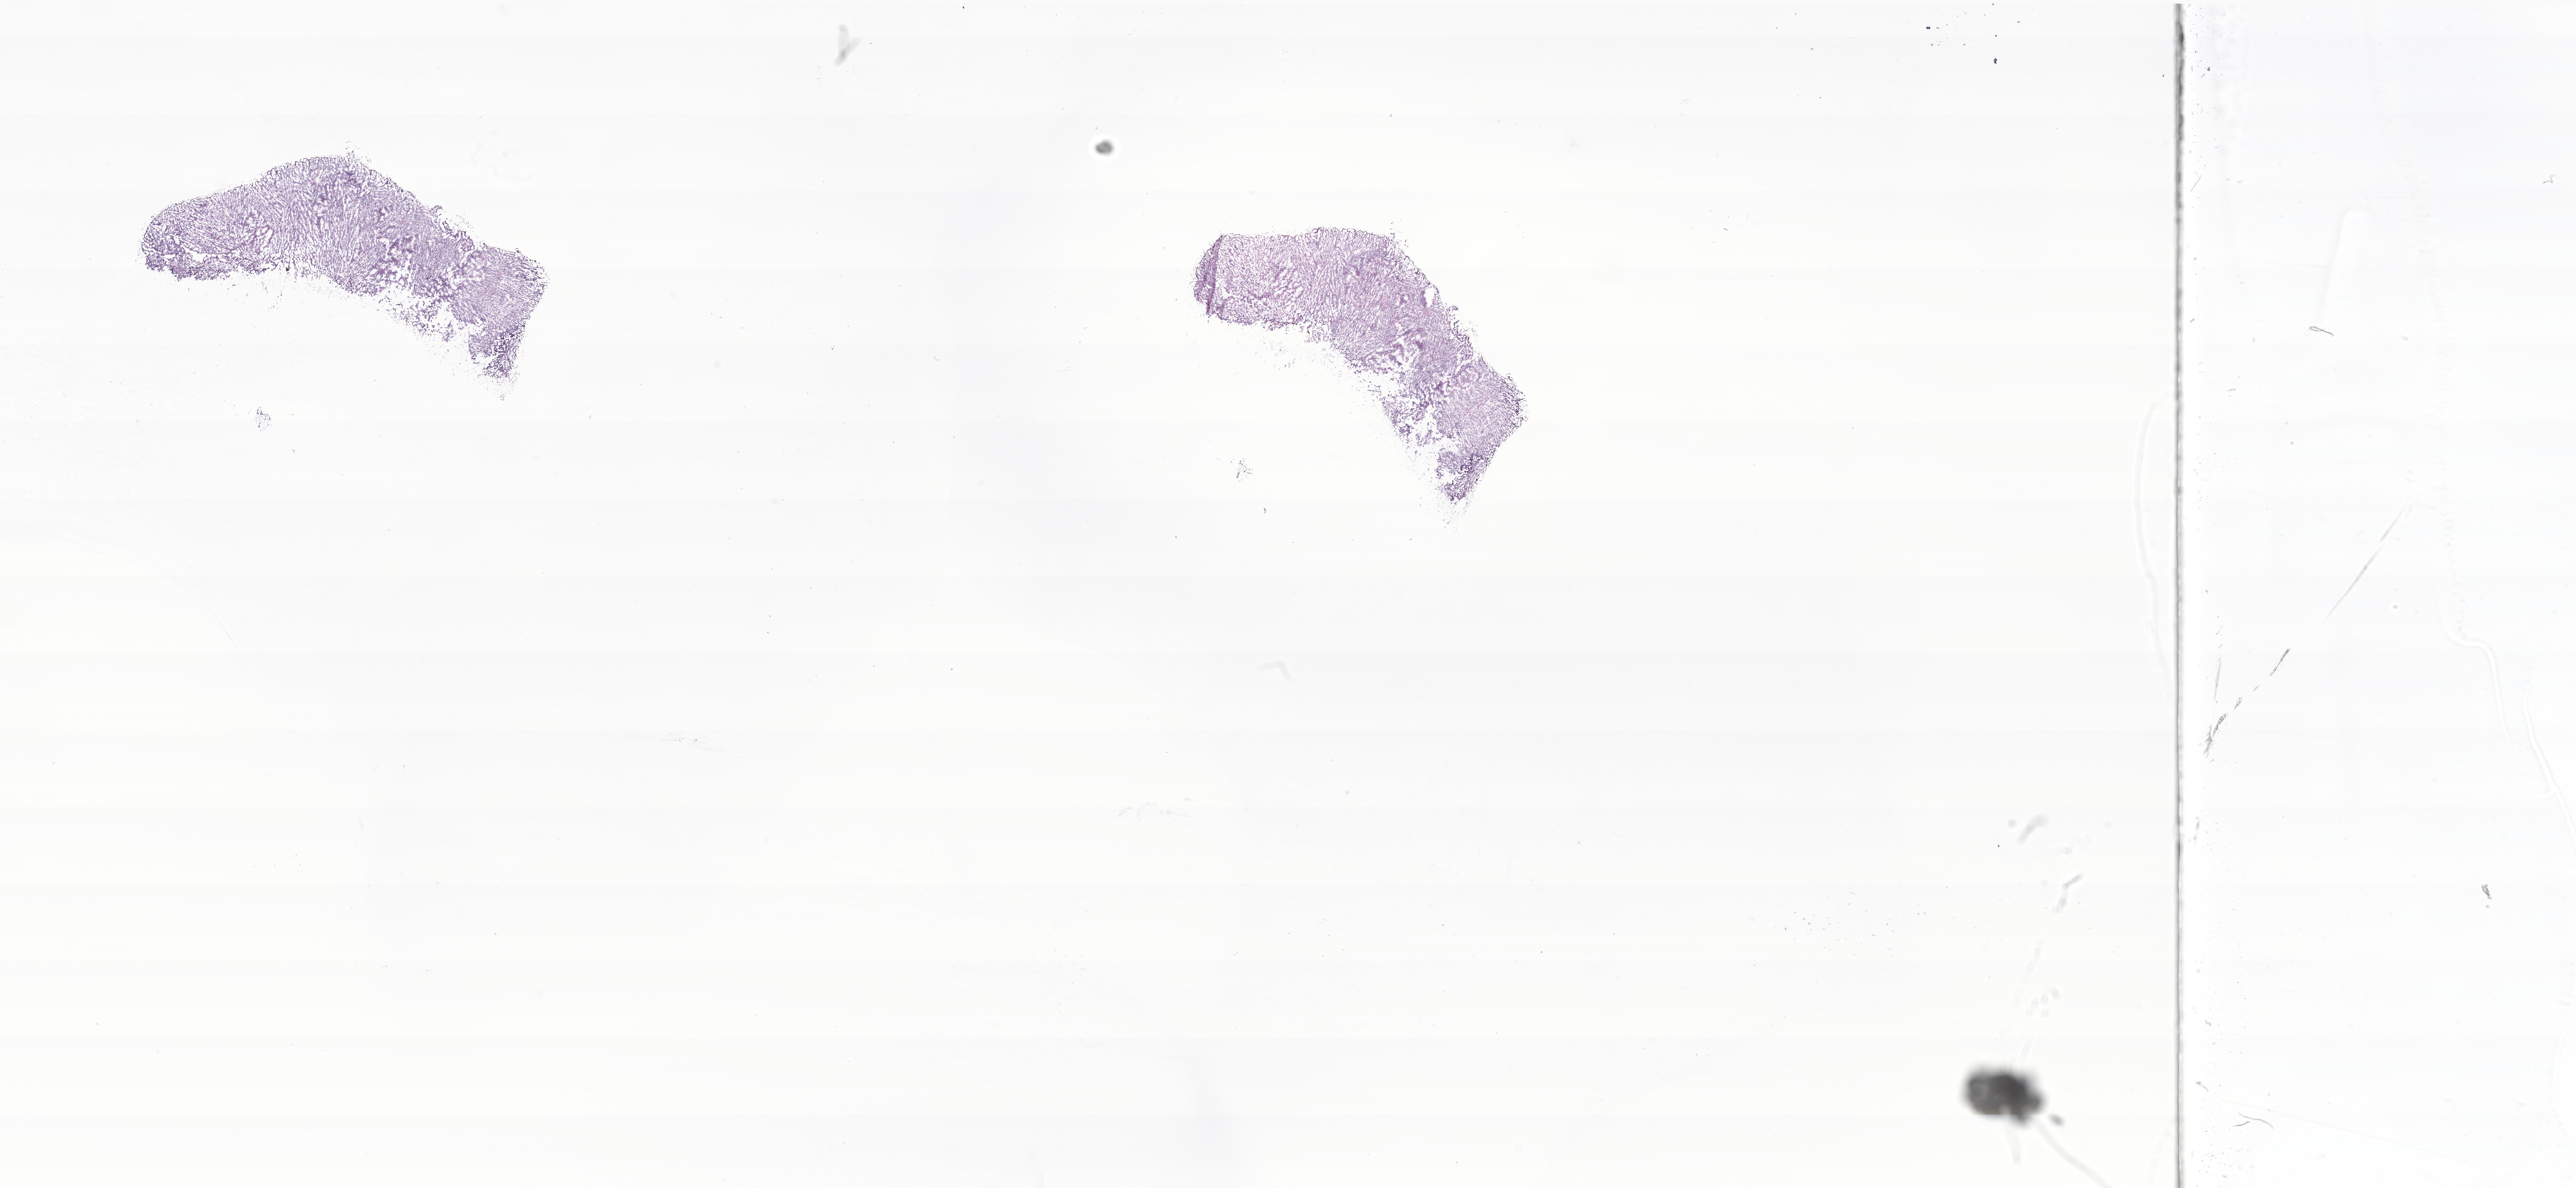
Digitized hematoxylin and eosin (H&E)-stained section of tumor tissue from the brain, a low-resolution overview of the entire scanned area, about 35.7 x 16.5 mm, cryosection (OCT / tissue freezing medium). Patient female; age 95 months (7 years 11 months).
Diagnosis: Neoplasm, malignant.